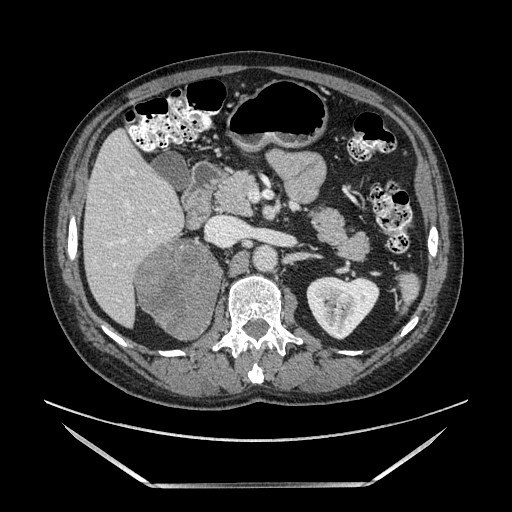
Contrast-enhanced abdominal CT, one axial slice. Slice 69 of 185 in the series (ordered by position). Soft-tissue window (W 400 / L 40 HU). 512 × 512 image matrix, field of view 440 × 440 mm. Male patient. Case-level facts recorded for this patient, not image findings: diagnosis: adrenocortical carcinoma; tumour side: right adrenal; tumour size at pathology: 10.3 cm; Ki-67 index: 20 %; stage (as recorded): 3.
Structures marked on this image (semi-automatic segmentation, software-assisted and operator-edited):
- mass: box from (x=135, y=239) to (x=218, y=338) px